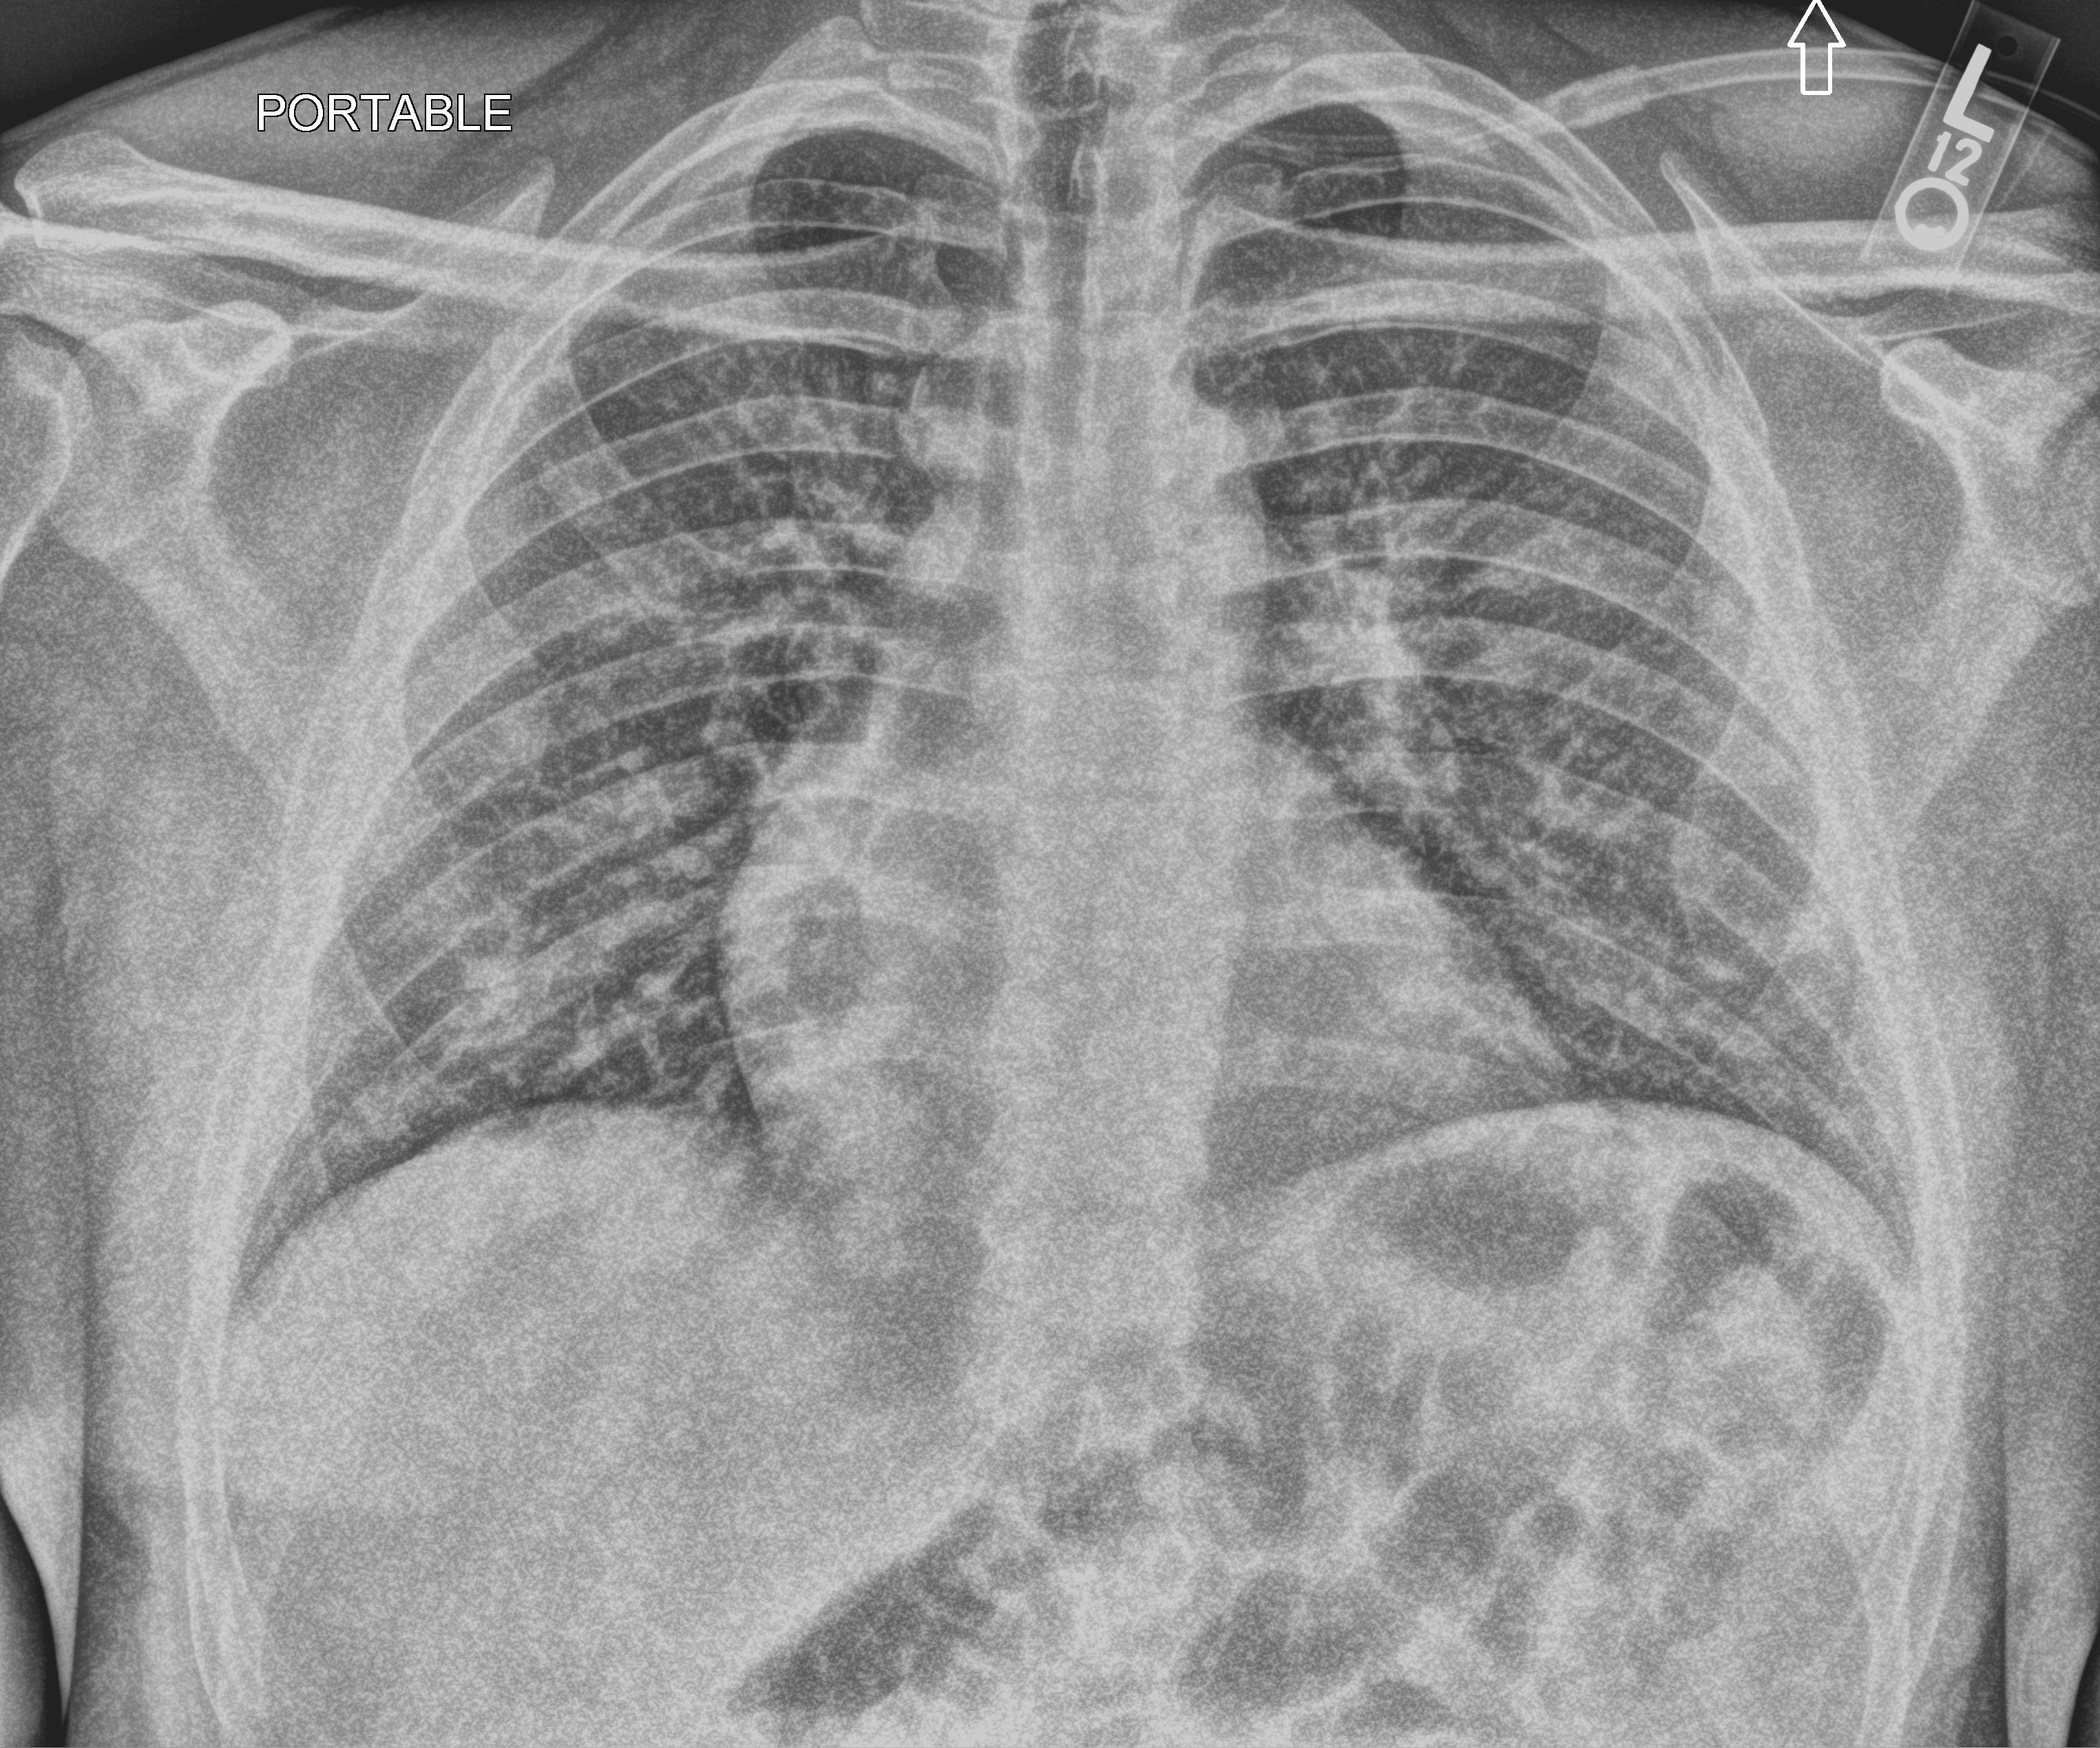
Bedside chest radiograph (computed radiography), anteroposterior (AP) projection. Male patient hospitalised with COVID-19, age 18–59 years.
Hospital-stay facts (about this admission, not read from this image; timing relative to this image not recorded): chronic kidney disease (admission record): no; mechanically ventilated during this hospital stay: no; admitted to intensive care during this hospital stay: no.